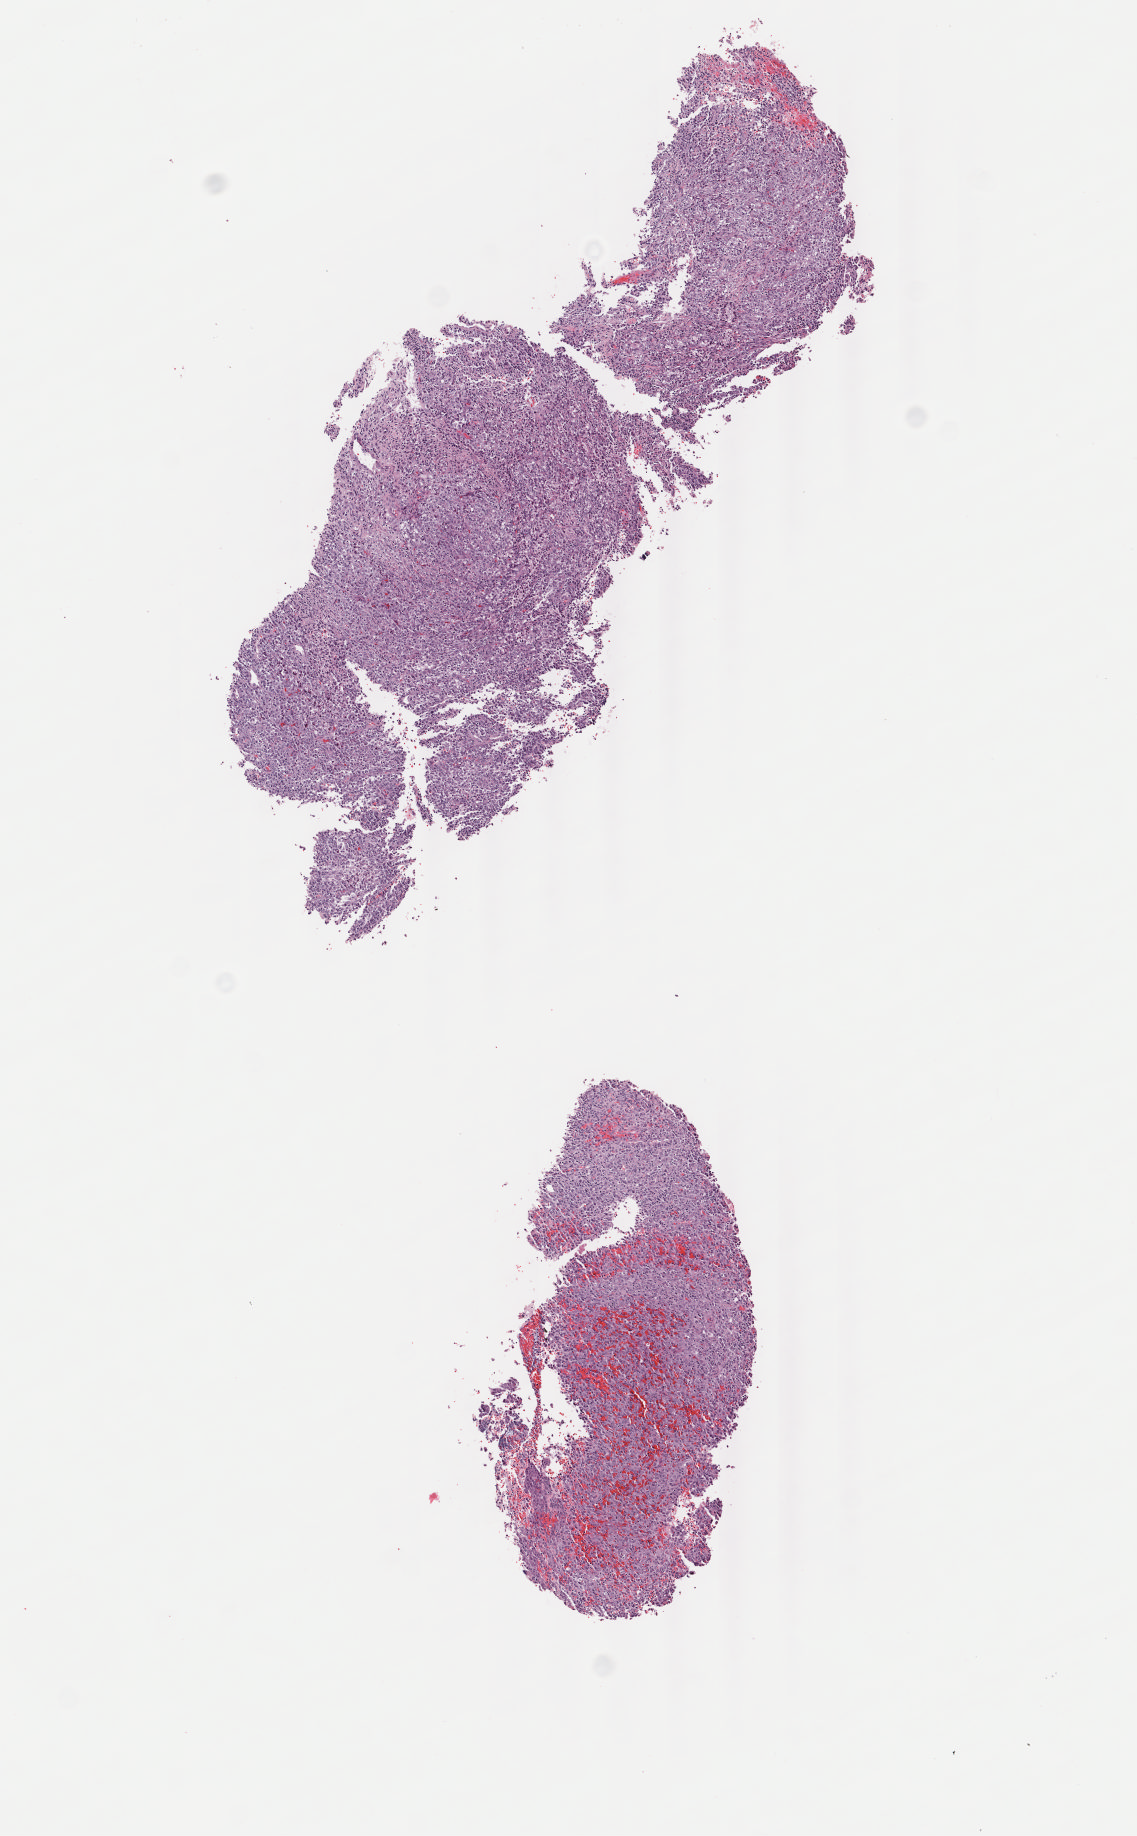
Digitized H&E tissue section (whole slide) — low-resolution overview of the scanned area, about 4.5 x 7.3 mm (slide scanned at 40x). Frozen section. Bladder, primary tumour sample. Patient: female, age at initial diagnosis 57 years. Histologic grade: high grade. Pathologist review of this section (percent, as recorded): tumour cells 85%, tumour nuclei 90%, normal cells 0%, stromal cells 10%, necrosis 5%. Infiltration values recorded for this section: lymphocyte infiltration 0%, monocyte infiltration 0%, neutrophil infiltration 0%.
Histologic diagnosis: Transitional cell carcinoma. AJCC pathologic stage: III (7th edition).